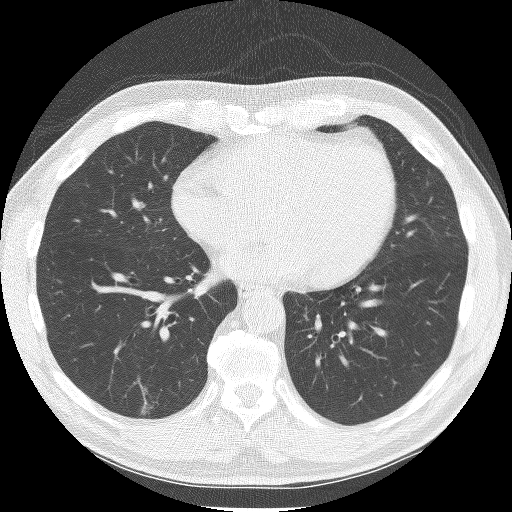
Low-dose screening chest CT, one axial slice. Slice 61 of 150 in the series (ordered by position). Lung window (W 1500 / L -600 HU). 2.5 mm slice thickness. 512 × 512 image matrix, field of view 335 × 335 mm.
Annotated regions visible in this slice (outlined manually by an expert reader):
- lesion 1 (tumor, lower lobe of right lung): bounding box <142,406,153,420> (left, top, right, bottom; pixels)